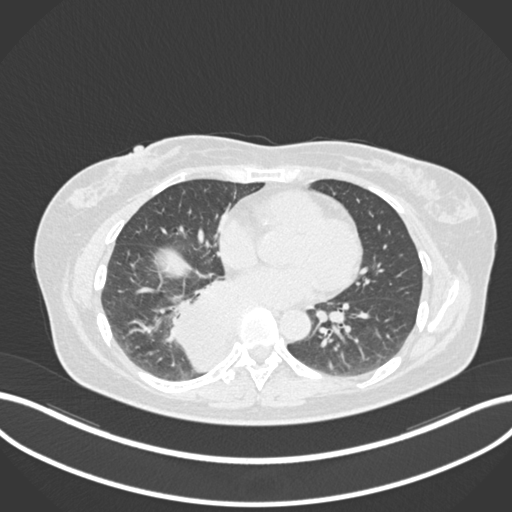
Chest CT, one axial slice; slice 570 of 677 in the series (ordered by position); 120 kVp; lung window (W 1500 / L -600 HU); 512 × 512 image matrix, field of view 400 × 400 mm. Patient: female, 54 years. Case-level facts recorded for this patient, not image findings: clinical TNM (as recorded): T4 N0 M0.
Structures marked on this image (bounding box drawn by a radiologist):
- lung tumour (recorded histology: adenocarcinoma): bounding box <165,273,242,379> (left, top, right, bottom; pixels)